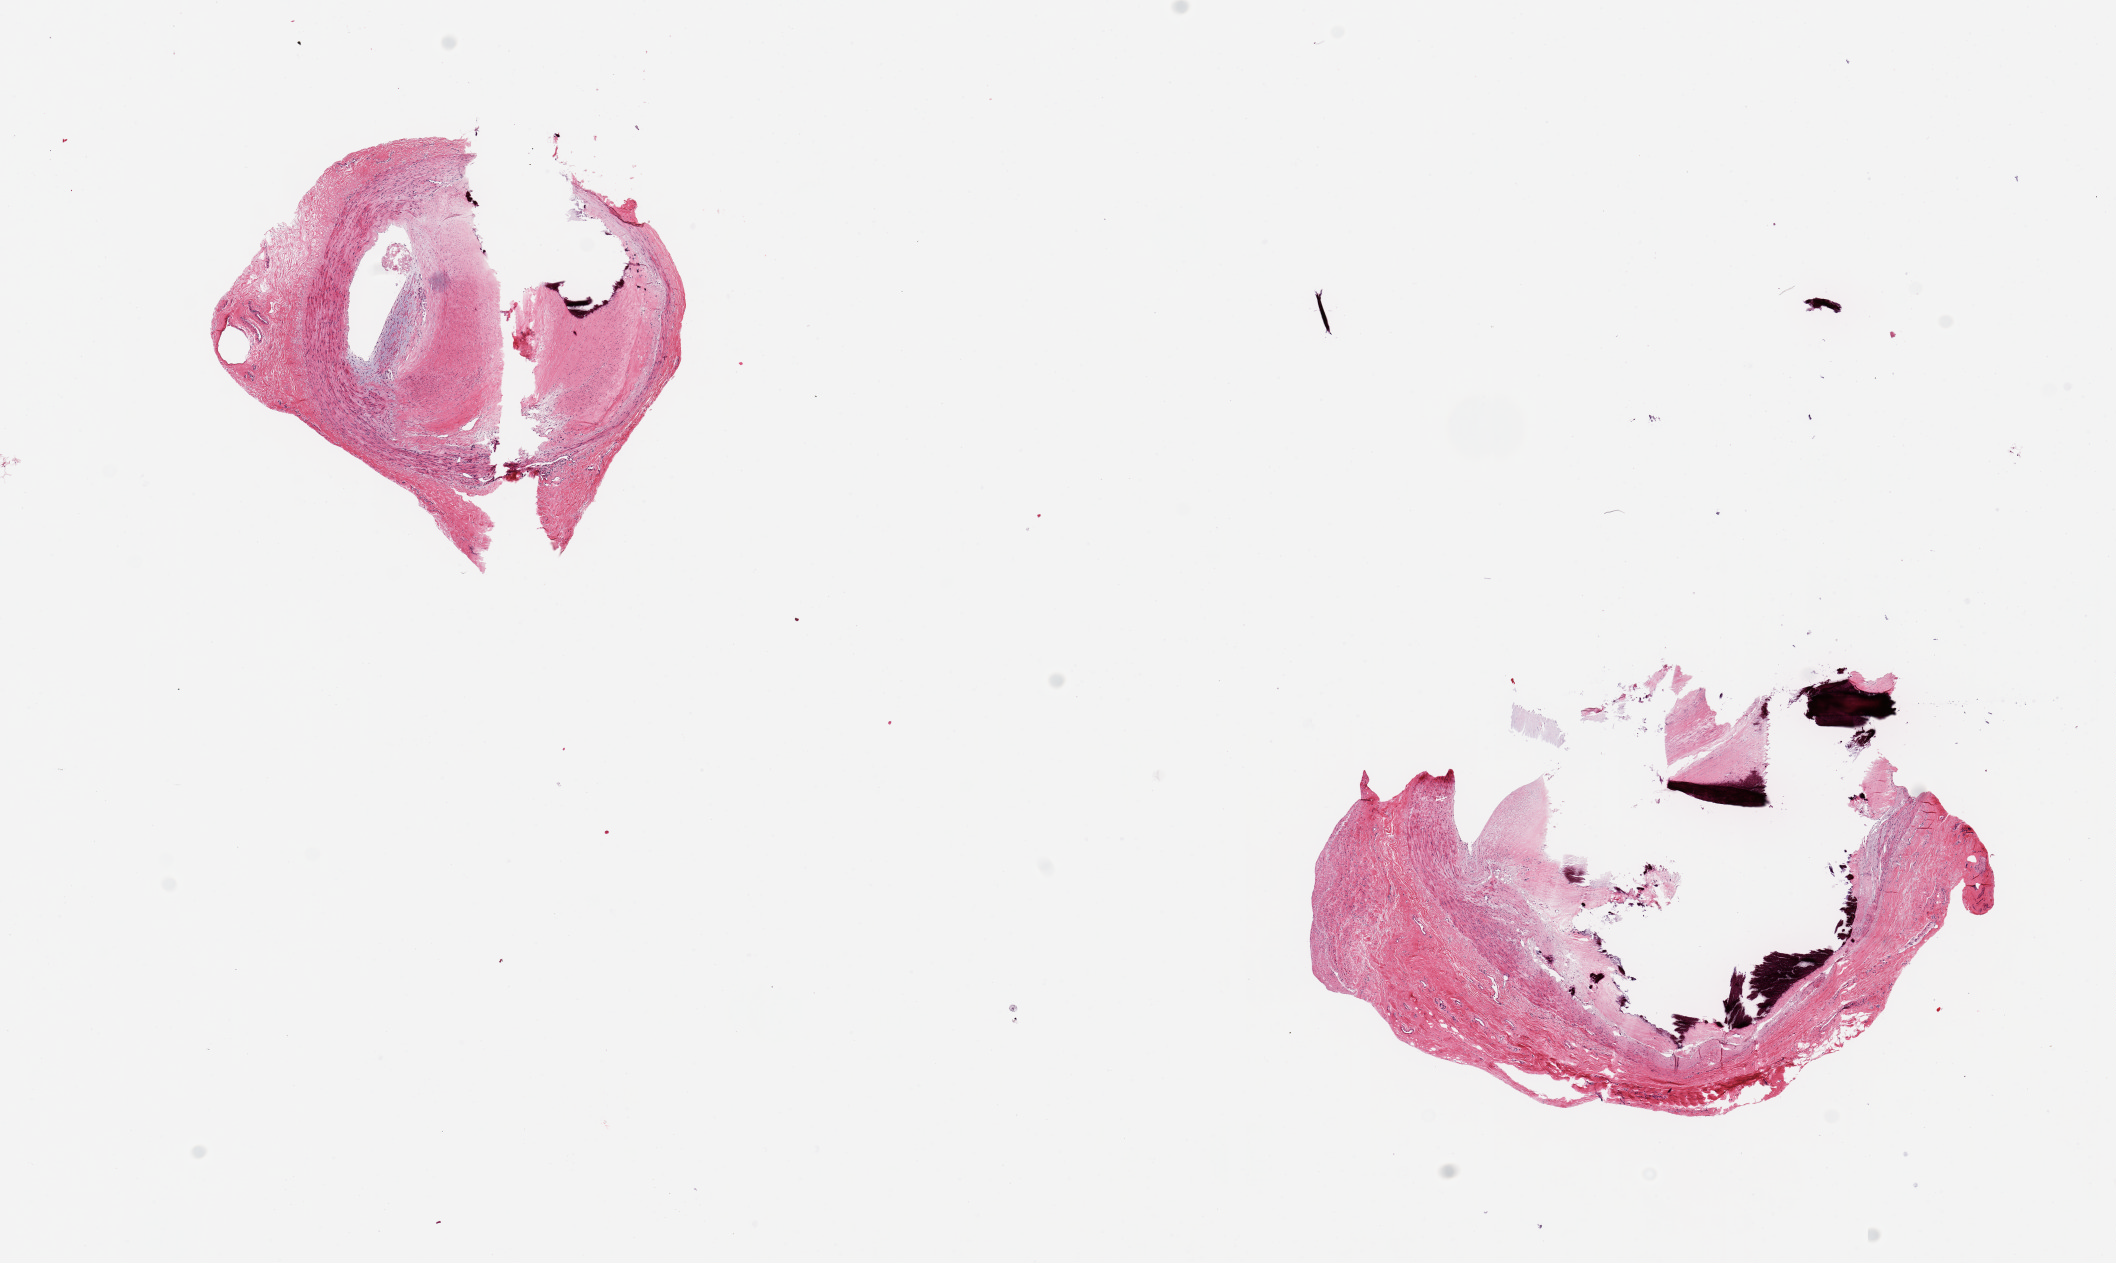
Digitized H&E-stained section — whole scanned area (about 16.7 x 10.0 mm) shown as a low-resolution overview; PAXgene-fixed paraffin-embedded (PFPE) section; target tissue: tibial artery; tissue donor sample. Donor sex: male.
Reviewer comment on this tissue sample: 2 pieces~4mm d; Subtotal occlusive atherosclerotic debris, calcified, in both.